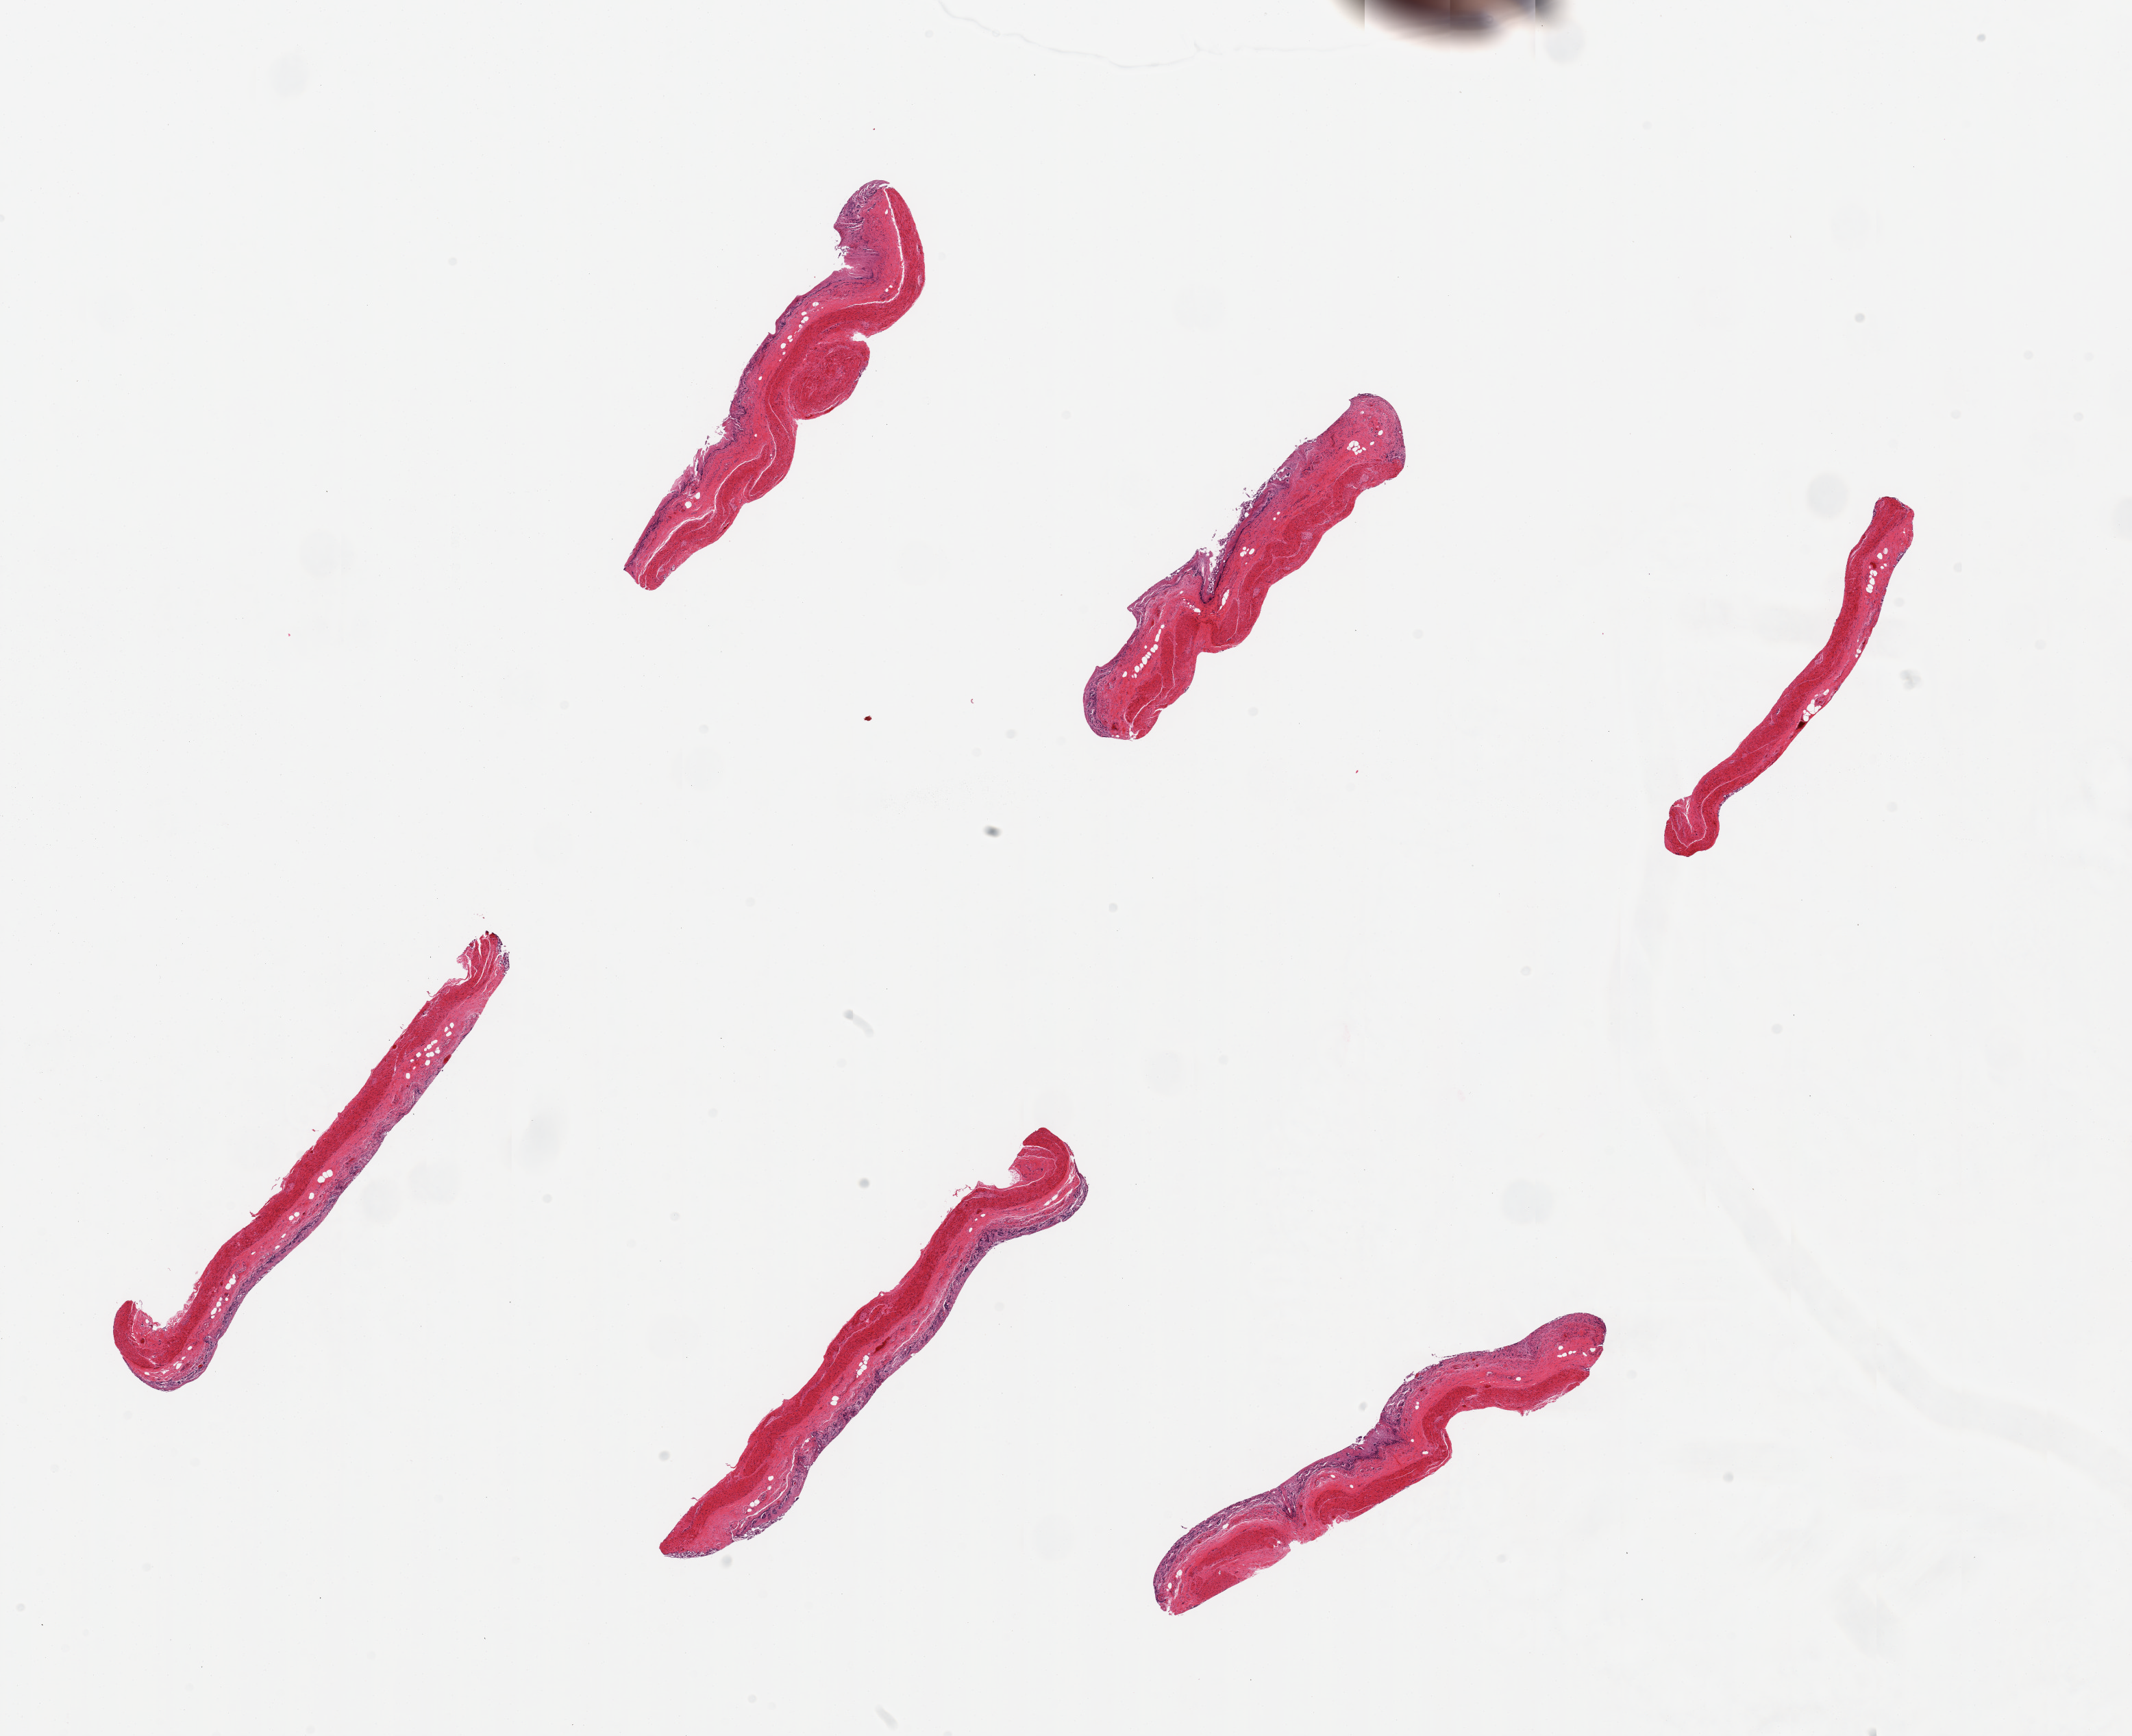
Whole-slide image, H&E stain, shown as a low-resolution overview of the whole scanned area (about 24.6 x 20.0 mm, acquisition: 20x scan), PAXgene-fixed, paraffin-embedded tissue, sampled site (target tissue): transverse colon, donor tissue sample. Donor: male.
Review note (as recorded): 6 pieces; predominantly full thickness, but mucosa is autolyzed.